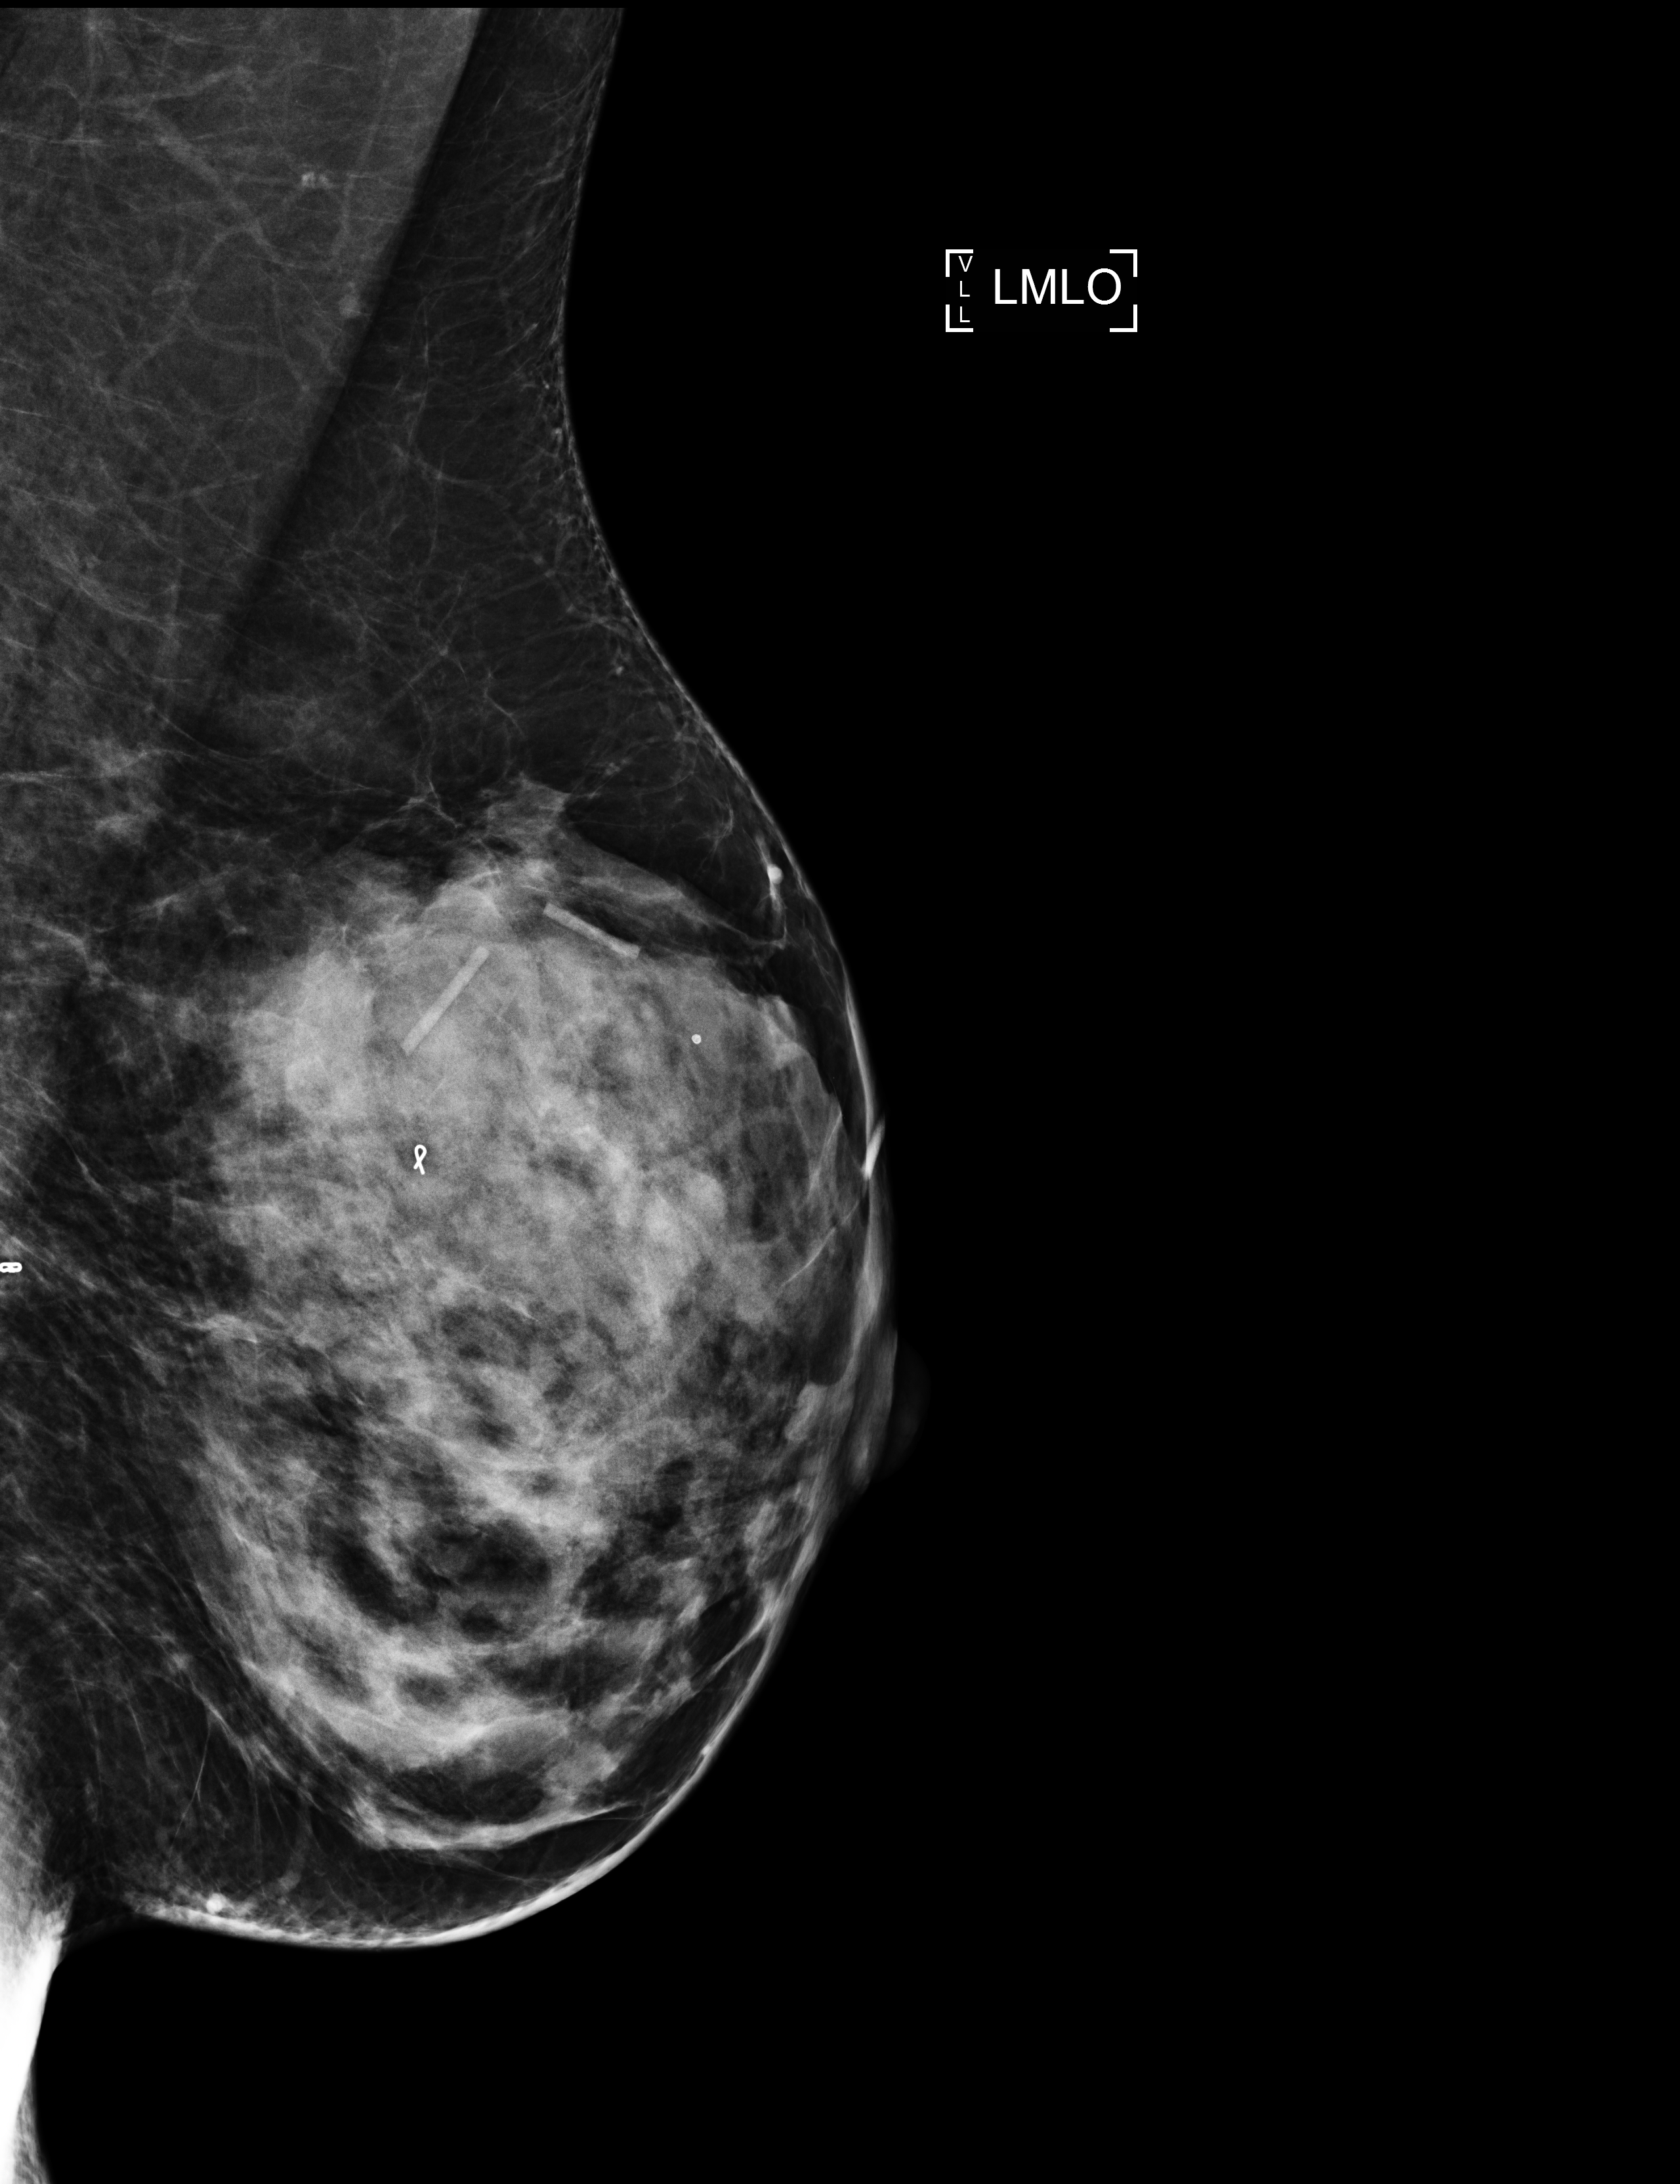
Screening examination, compressed breast thickness 58 mm, system: Selenia Dimensions. Patient: female, 48 years.
Image type: full-field digital mammogram. Breast: left. Projection: MLO view.